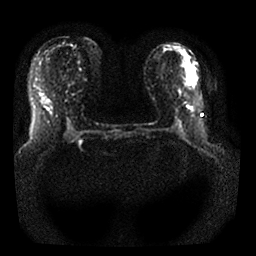
Breast MRI, one axial slice; position 13 of 25 along the scan axis; diffusion-weighted series; image 2 of 4 stored at this slice position (different b-values; order by instance number); 1.5 T; 4 mm slice thickness; 256 × 256 image matrix, field of view 320 × 320 mm. Female patient.
Structures marked on this image (manually delineated by an expert):
- tumour on diffusion-weighted imaging: box from (x=188, y=77) to (x=192, y=85) px